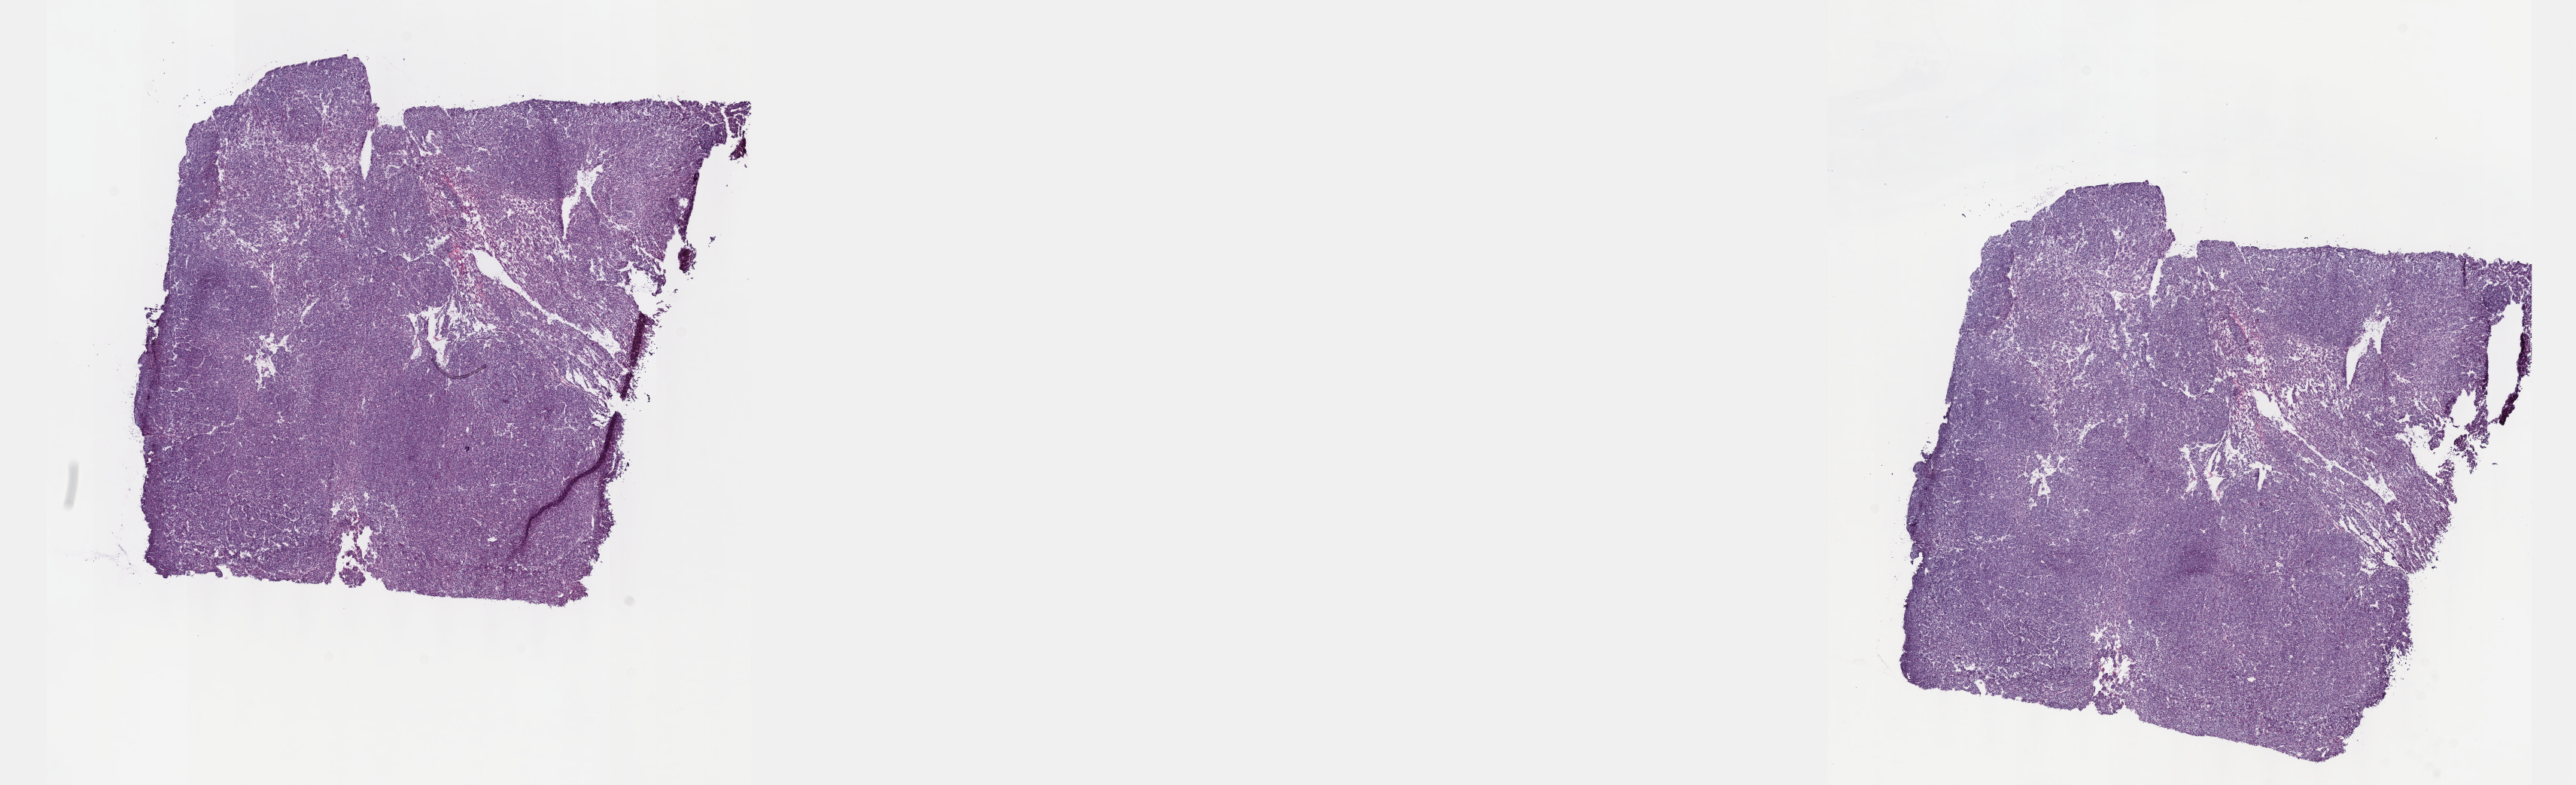
Whole-slide histology image, Hematoxylin and eosin (H&E) stained, shown as a low-resolution overview of the whole scanned area (about 27.7 x 8.4 mm, acquisition: 40x scan); frozen section; sample: primary tumour, thymus. Patient: female, age at initial diagnosis 75 years. Composition of this section per pathologist review: tumour cells 99%, tumour nuclei 99%, normal cells 0%, stromal cells 1%, necrosis 0%. Infiltration values recorded for this section: lymphocyte infiltration 0%, monocyte infiltration 0%, neutrophil infiltration 0%.
* pathologic diagnosis: Thymoma, type A, malignant